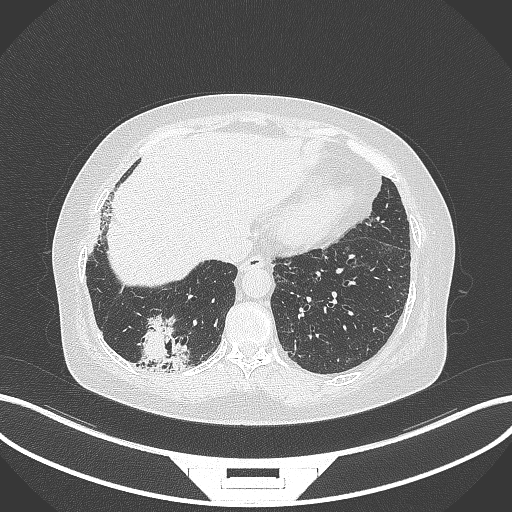
Chest CT, one axial slice. Position 41 of 296 along the scan axis. 120 kVp. Lung window (W 1500 / L -600 HU). 1 mm slice thickness. 512 × 512 image matrix, field of view 400 × 400 mm. Patient: female, 65 years. Case-level facts recorded for this patient, not image findings: clinical TNM (as recorded): T2b N1 M0.
Annotated regions visible in this slice (rectangle marked by the reading radiologist):
- lung tumour (recorded histology: adenocarcinoma): box from (x=132, y=312) to (x=191, y=371) px